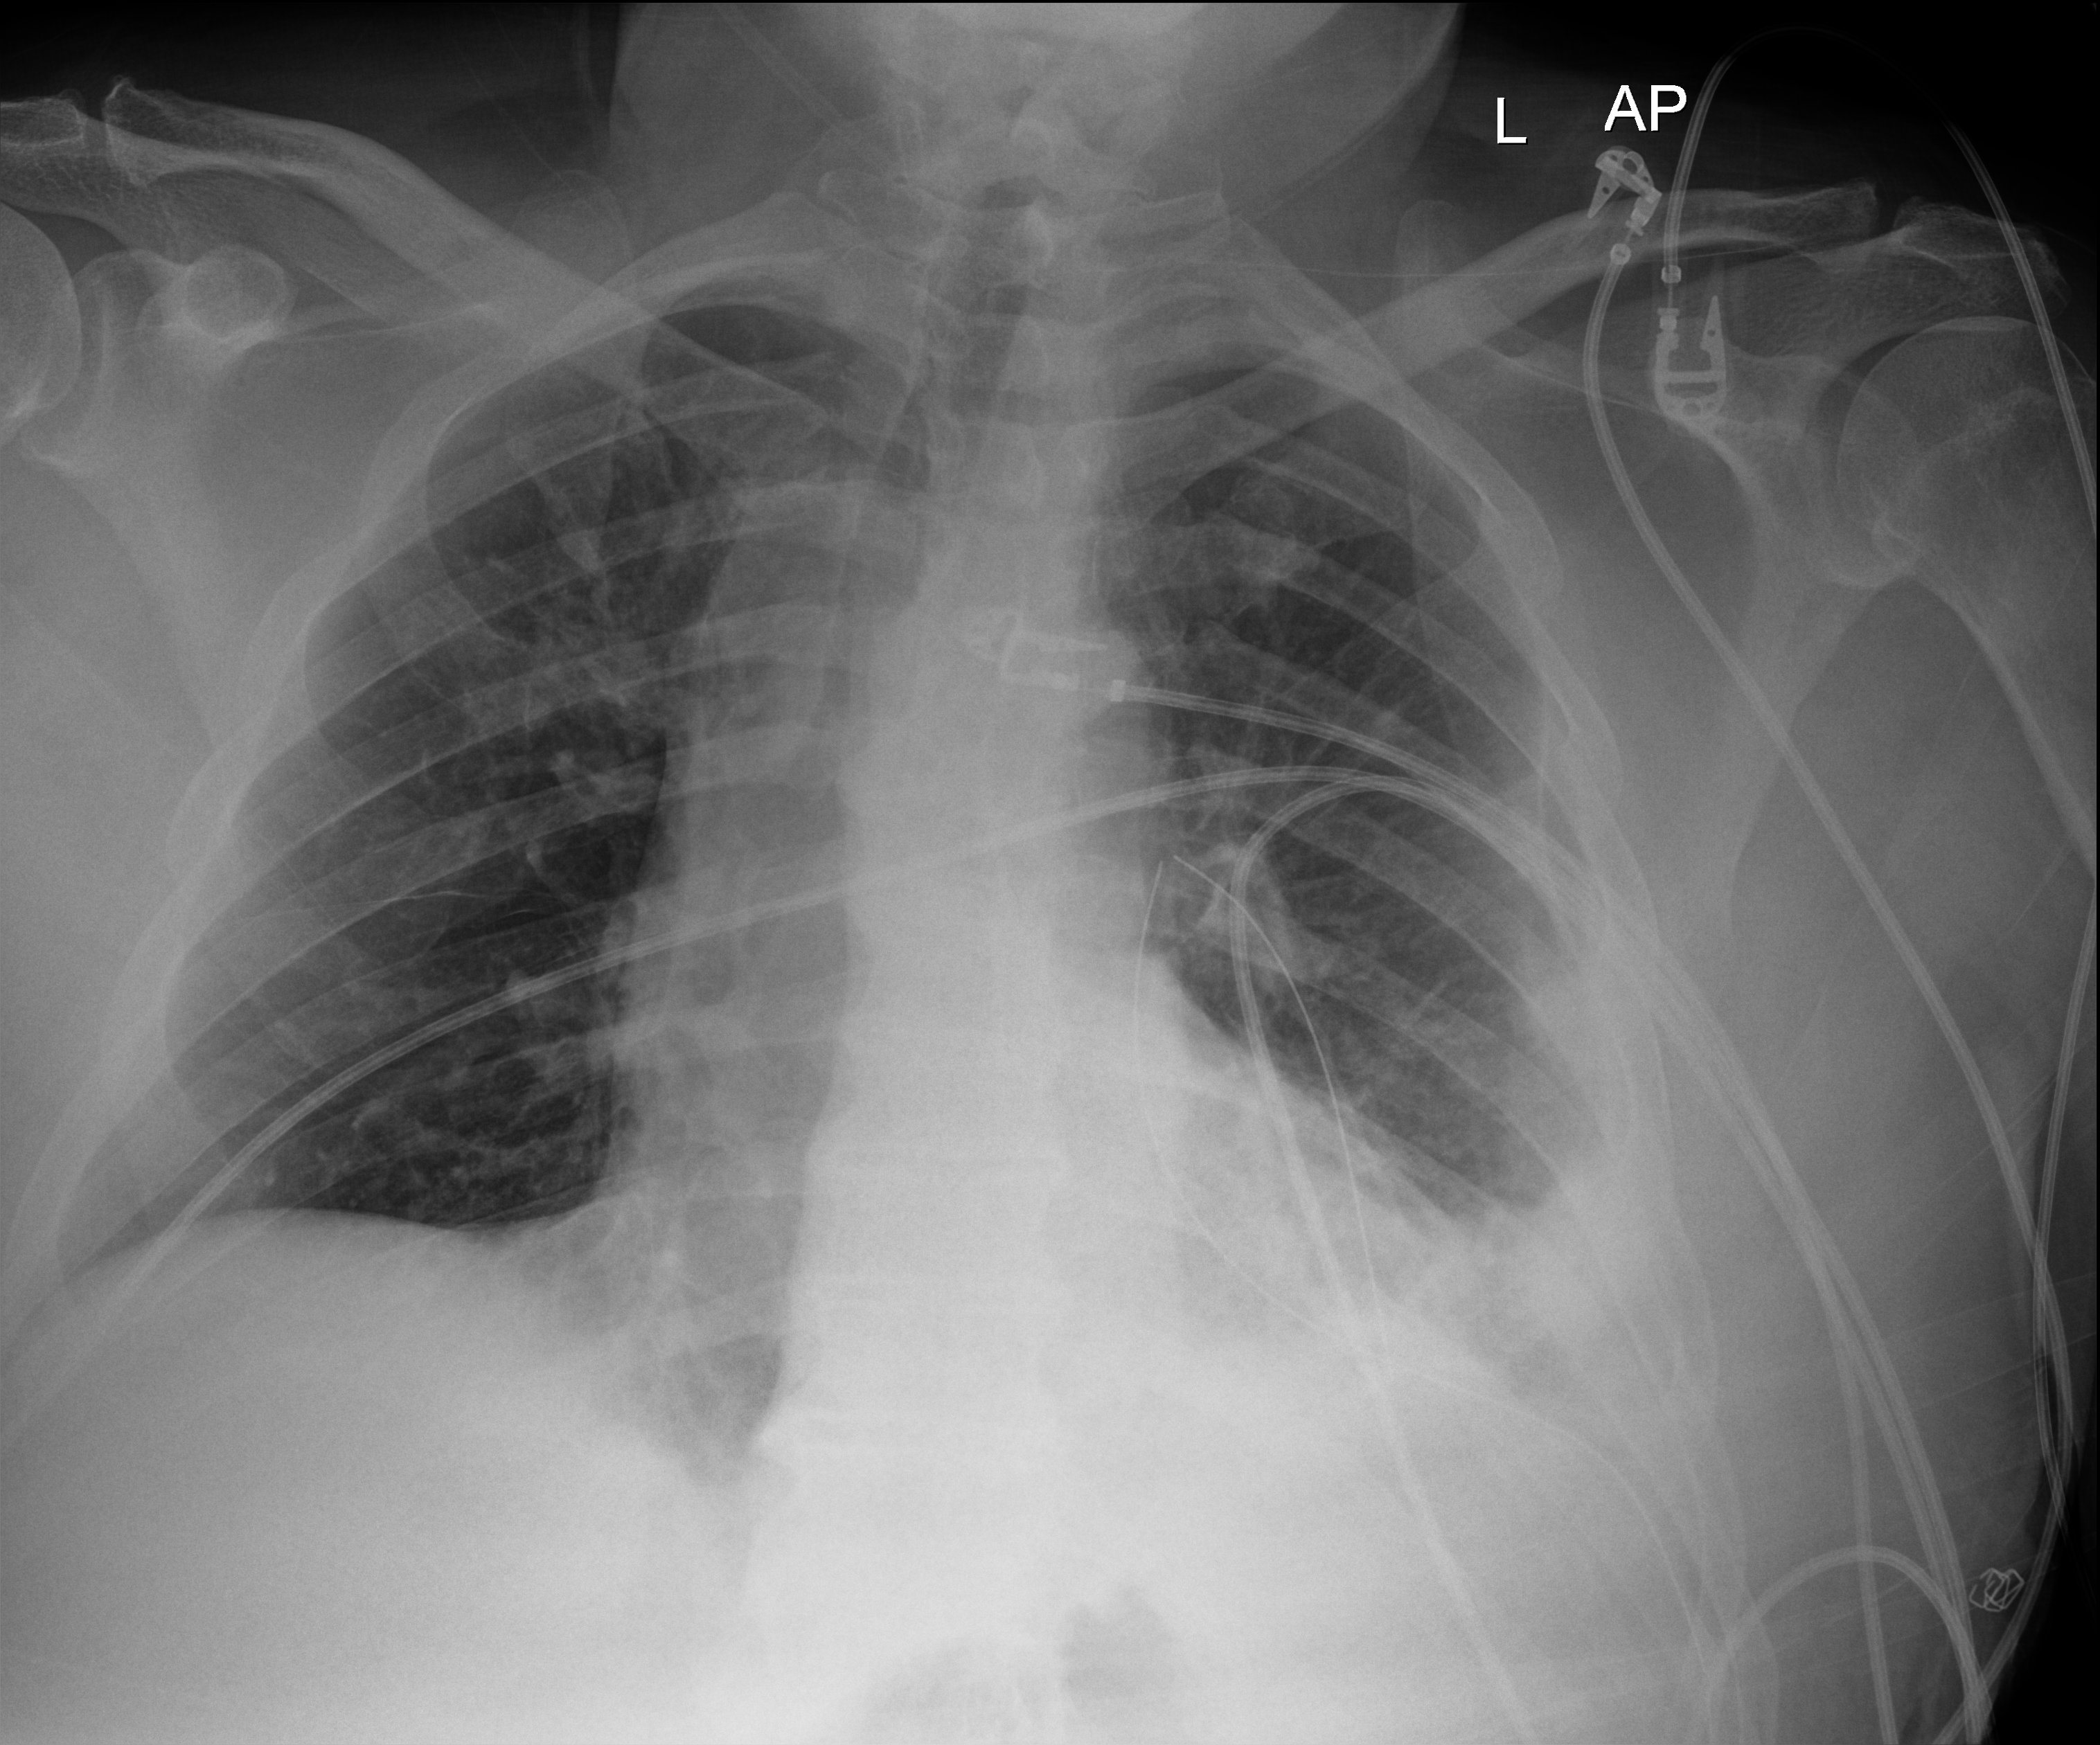
Portable chest radiograph, anteroposterior (AP) projection. Patient hospitalised with COVID-19; male, aged 18–59 years.
Admission-level facts for this patient (not findings on this image; timing relative to this image not recorded): admitted to intensive care during this hospital stay: no.